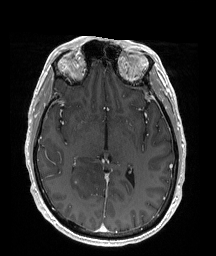
Brain MRI from a brain-tumour surgery series, one axial slice; slice 101 of 176 in the series (ordered by position); T1-weighted post-contrast; 1 mm slice thickness; 216 × 256 image matrix, field of view 211 × 250 mm. Case-level facts recorded for this patient, not image findings: histopathology: Oligodendroglioma; WHO grade: 2; IDH mutation: yes; tumour location: Right Parietal.
Structures marked on this image (manually delineated by an expert):
- tumour: bounding box (x1, y1, x2, y2) in pixels: (70, 153, 111, 194)